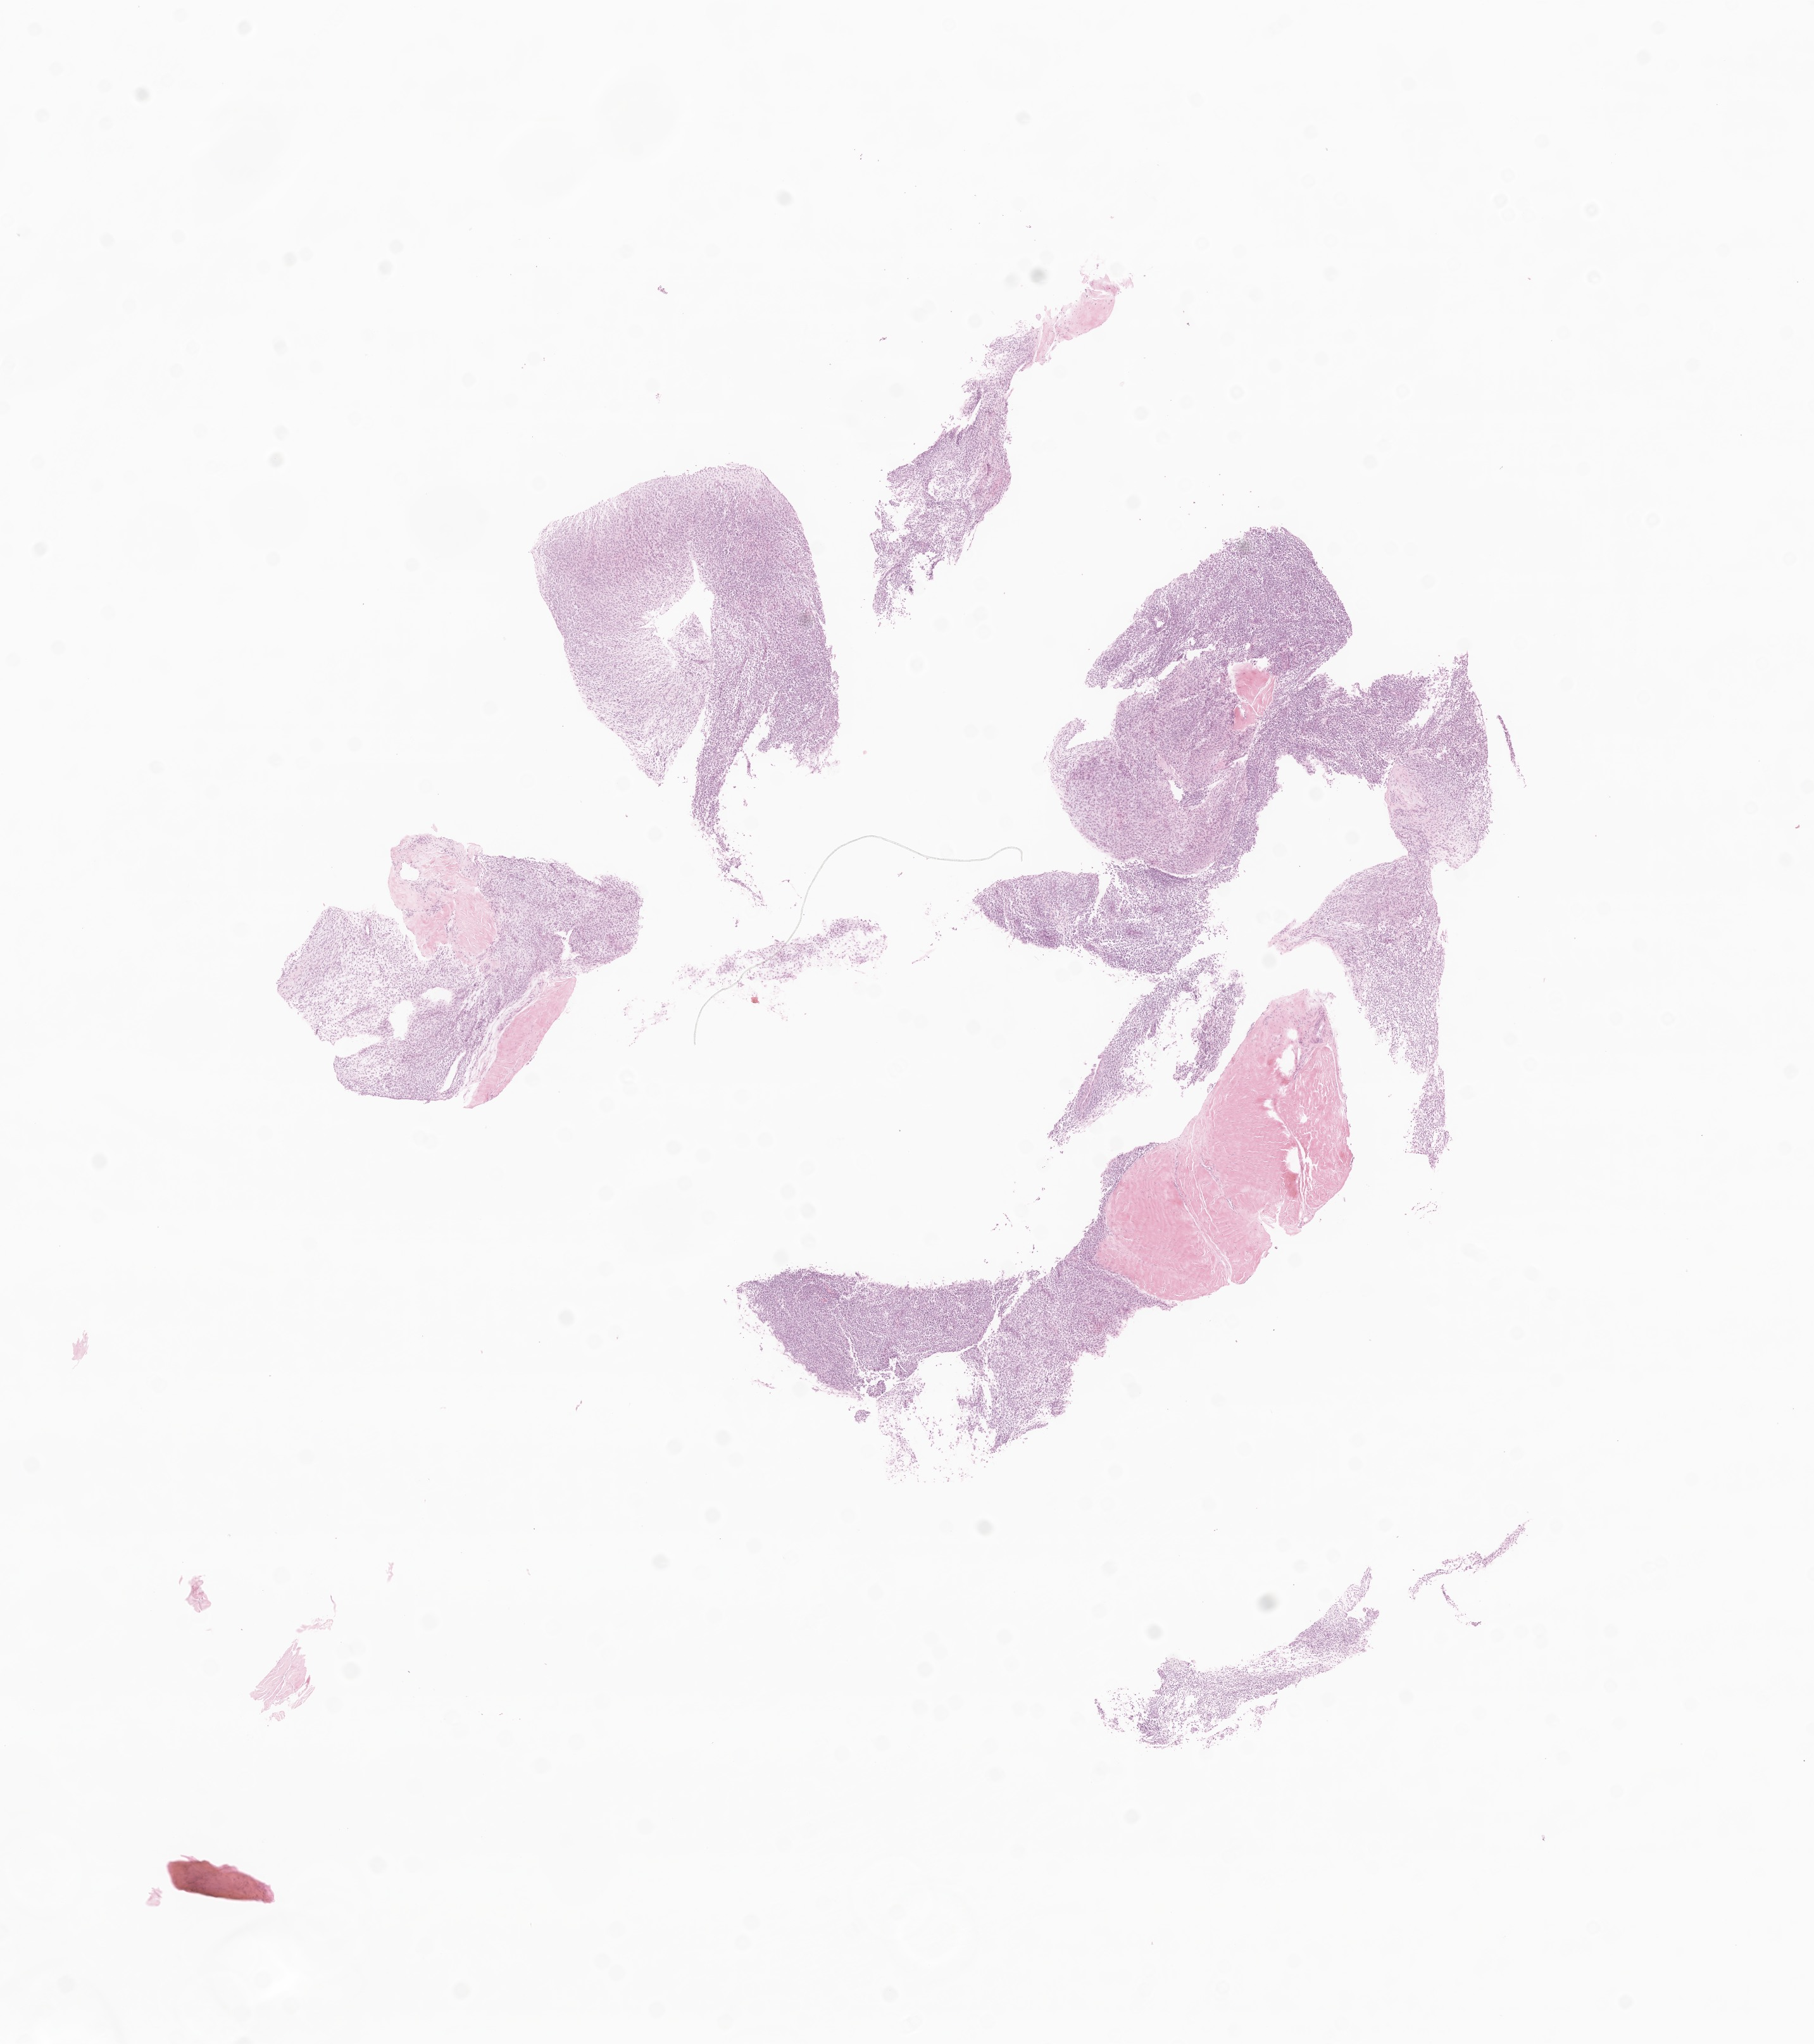
Hematoxylin and eosin (H&E) whole-slide image of tumor tissue from the soft tissue — shown as a low-resolution overview of the whole scanned area (about 12.1 x 13.6 mm); FFPE section. Patient male; age 190 months (15 years 10 months).
* recorded diagnosis: Sarcoma, NOS